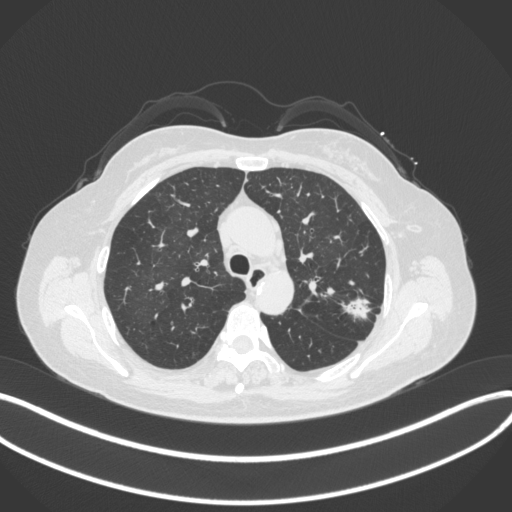
Chest CT, one axial slice. Slice 242 of 330 in the series (ordered by position). Reconstruction kernel B31f. Lung window (W 1500 / L -600 HU). 512 × 512 image matrix. Female patient, age 60 years. Case-level facts recorded for this patient, not image findings: clinical TNM (as recorded): T1c N0 M0.
Structures marked on this image (rectangle marked by the reading radiologist):
- lung tumour (recorded histology: adenocarcinoma): bounding box [x1, y1, x2, y2] px = [339, 290, 375, 325]